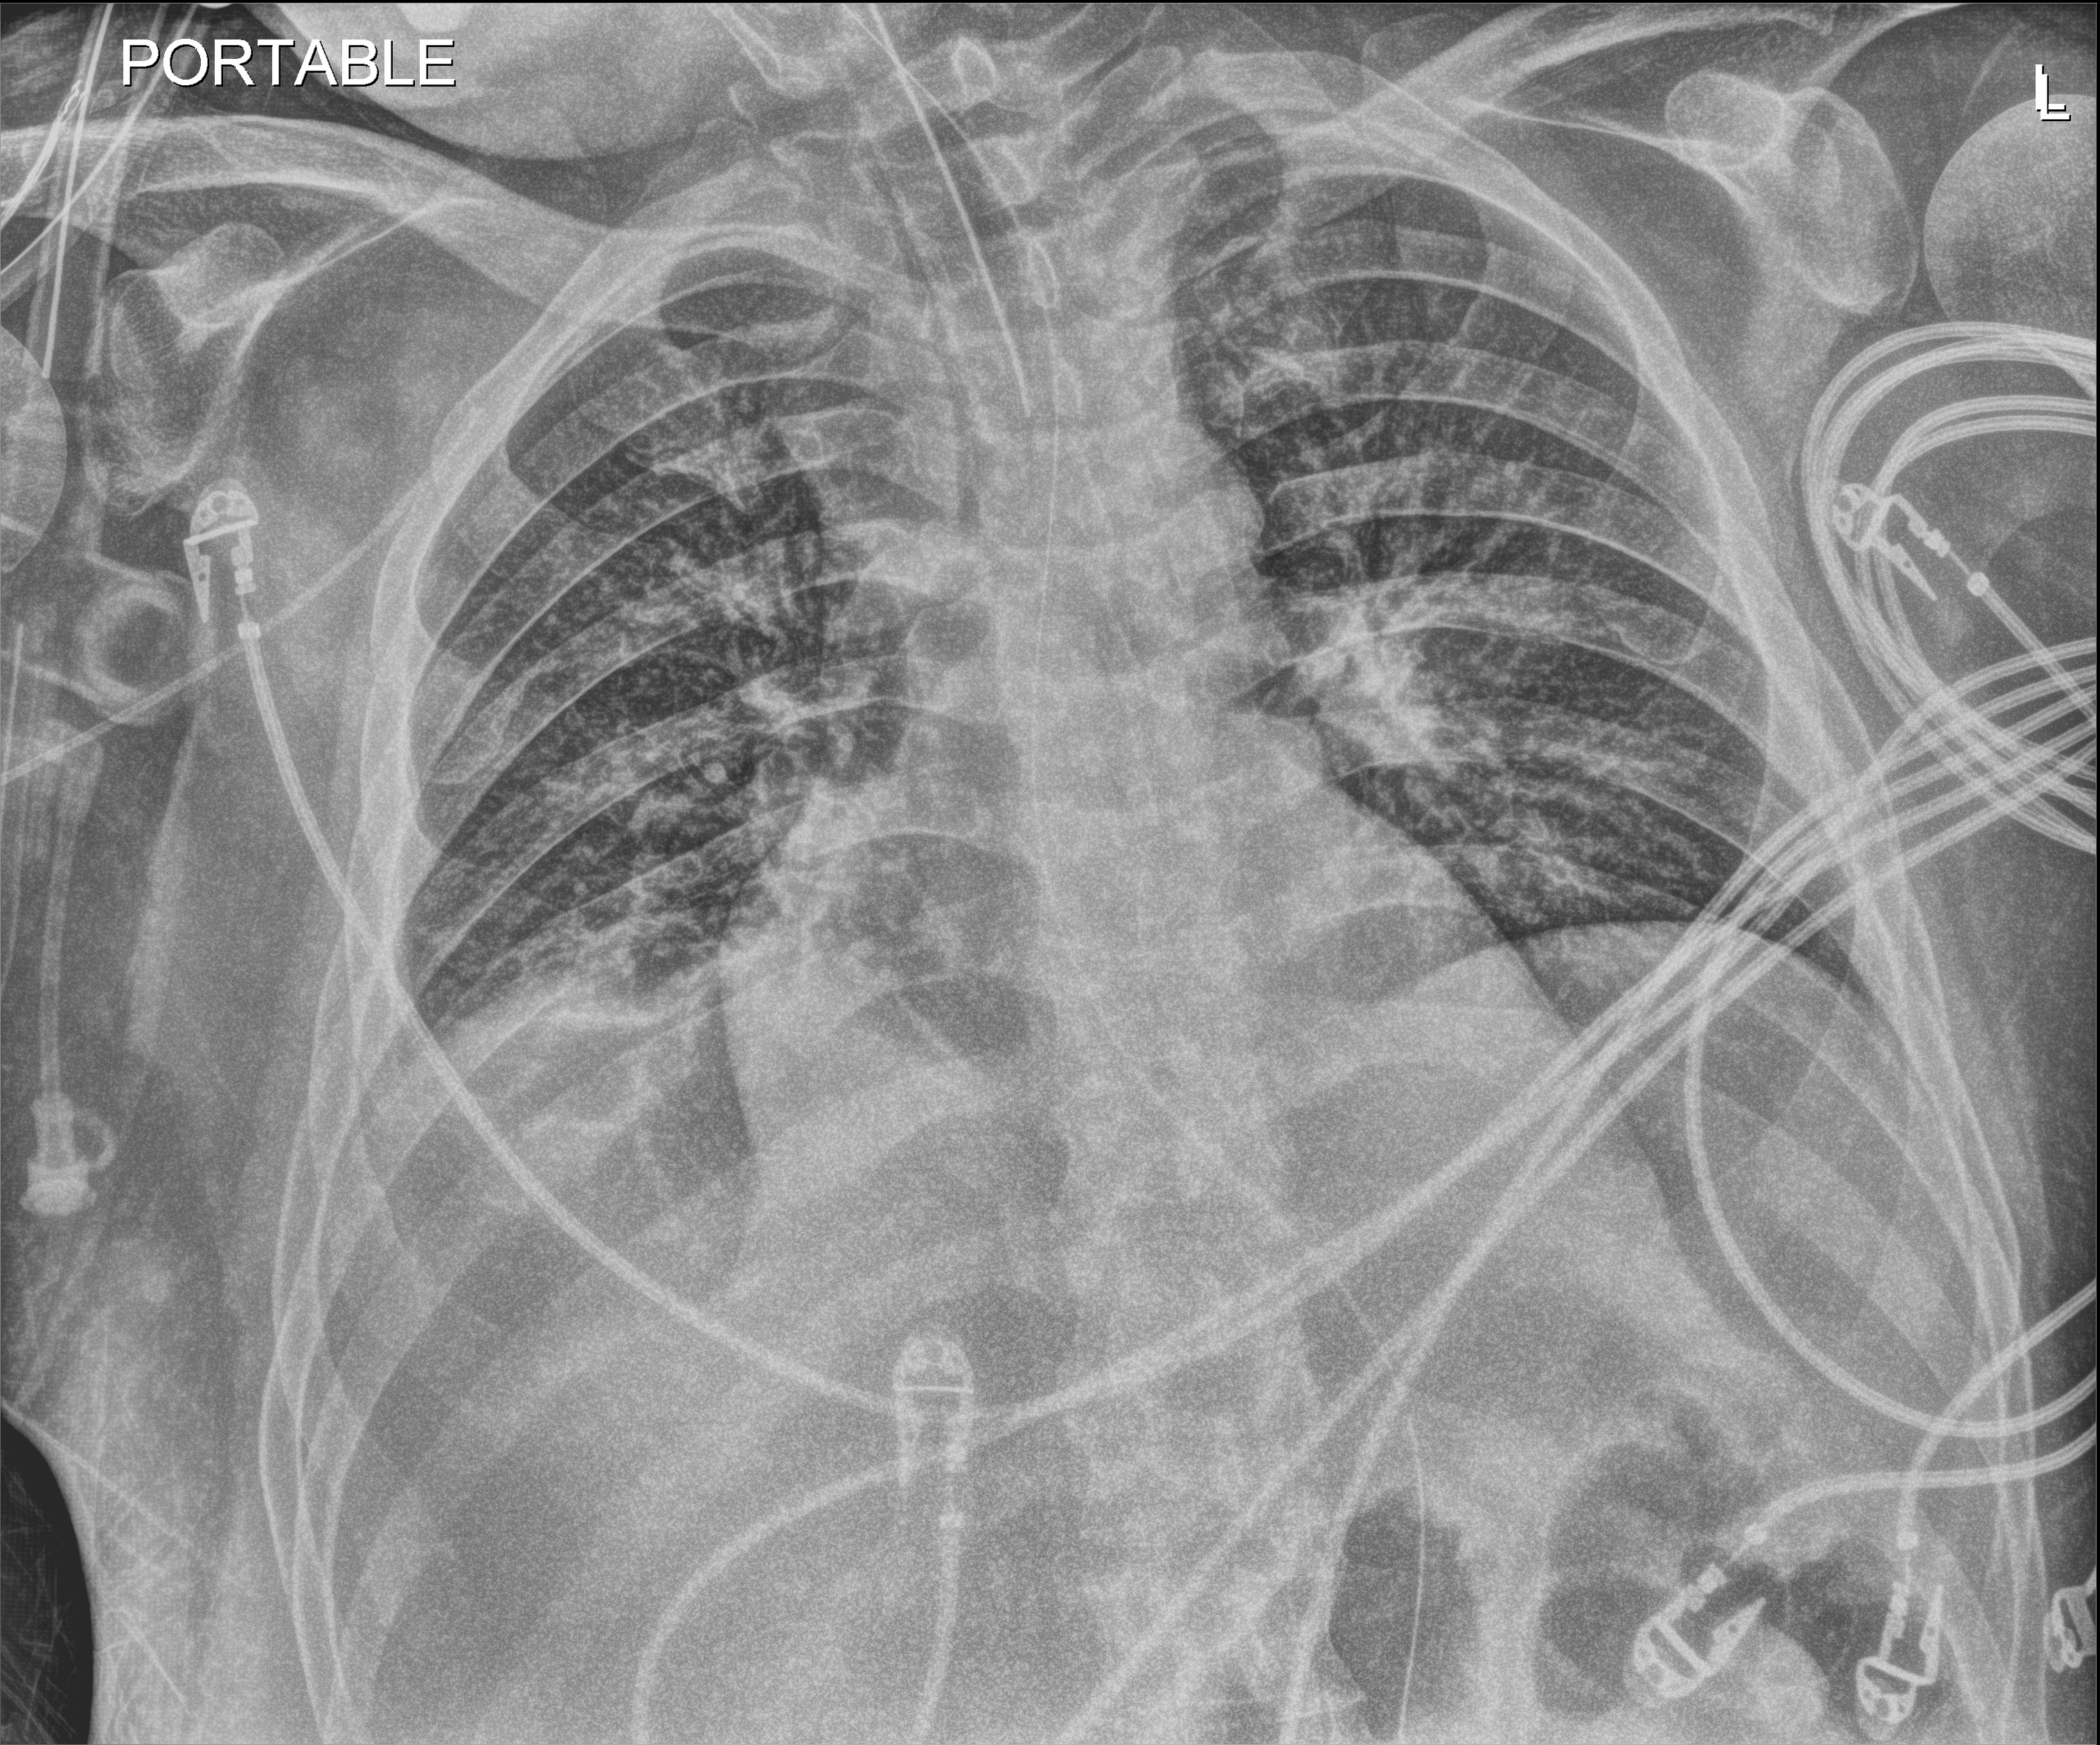
Portable chest radiograph; anteroposterior (AP) projection. Male patient hospitalised with COVID-19, age 18–59 years.
Hospital-stay facts (about this admission, not read from this image; timing relative to this image not recorded):
- length of hospital stay: 65 days